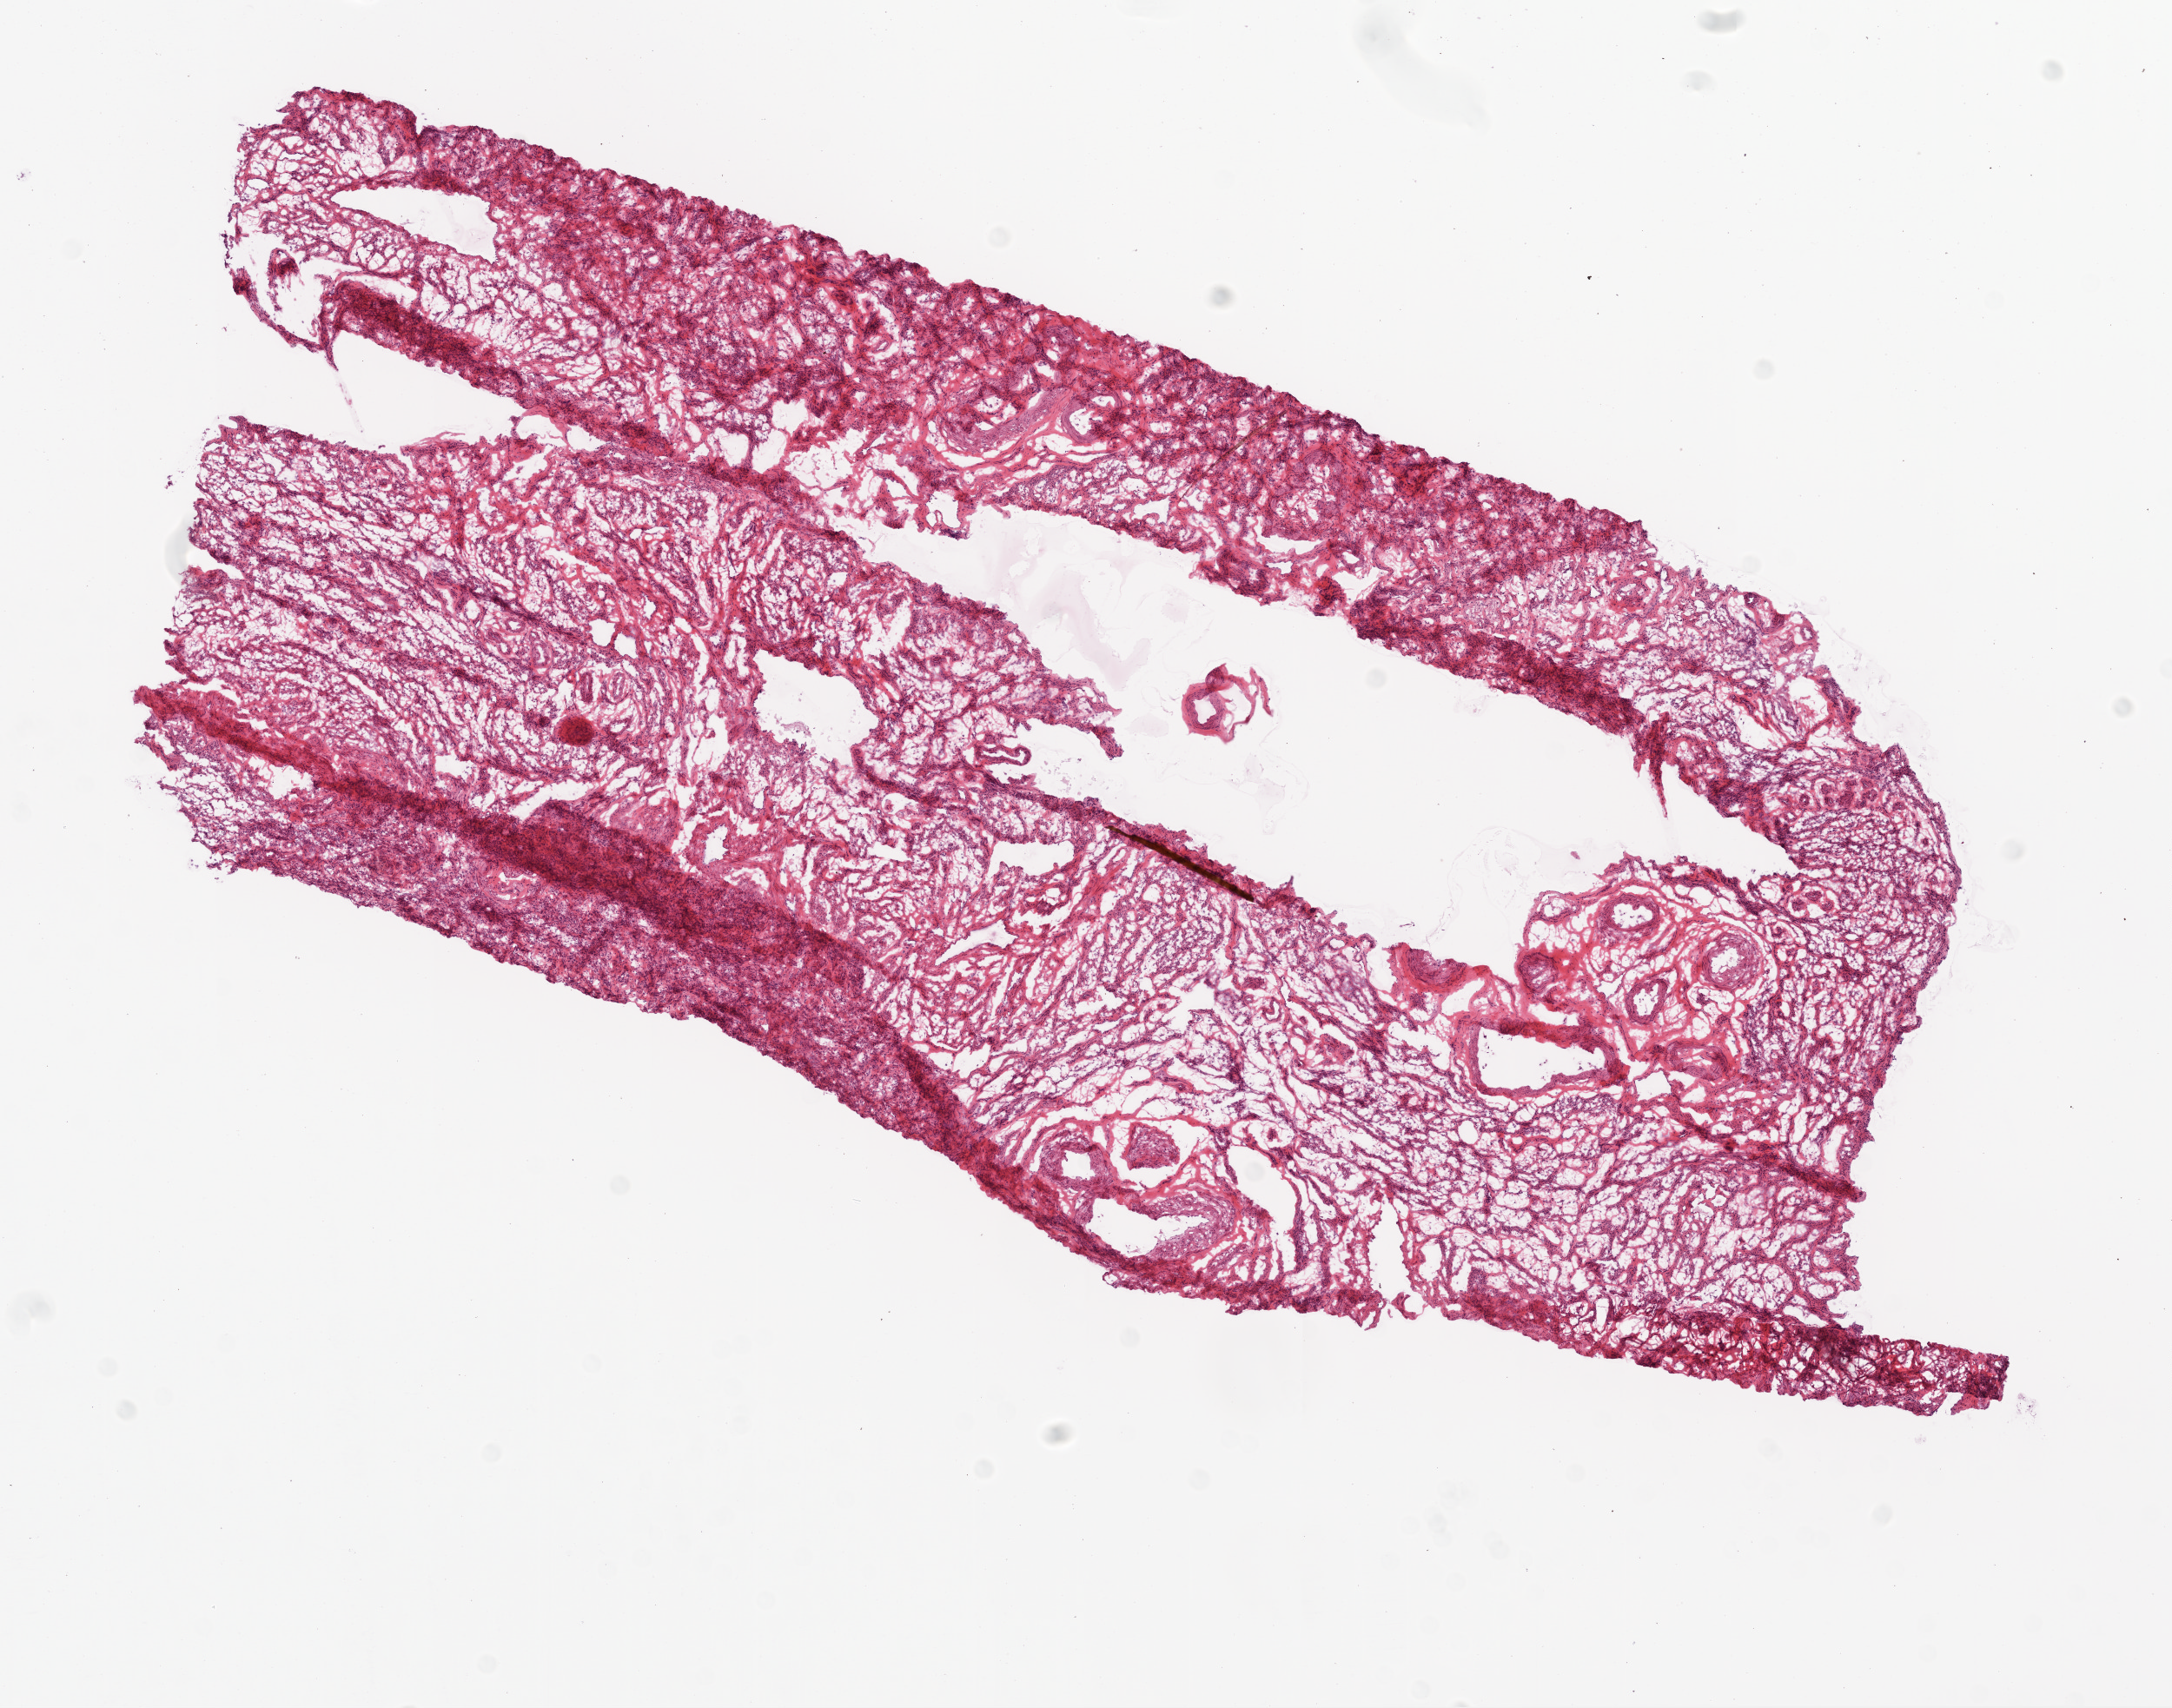
Whole-slide histology image, H&E-stained, low-resolution overview of the scanned area, about 10.0 x 7.9 mm (slide scanned at 20x), frozen section from the top of the tissue portion, ovary, solid tissue normal (non-tumour tissue) sample. Patient: female, age at initial diagnosis 67 years.
This section: solid tissue normal sample (biorepository sample class). Patient diagnosis: Serous cystadenocarcinoma, NOS.